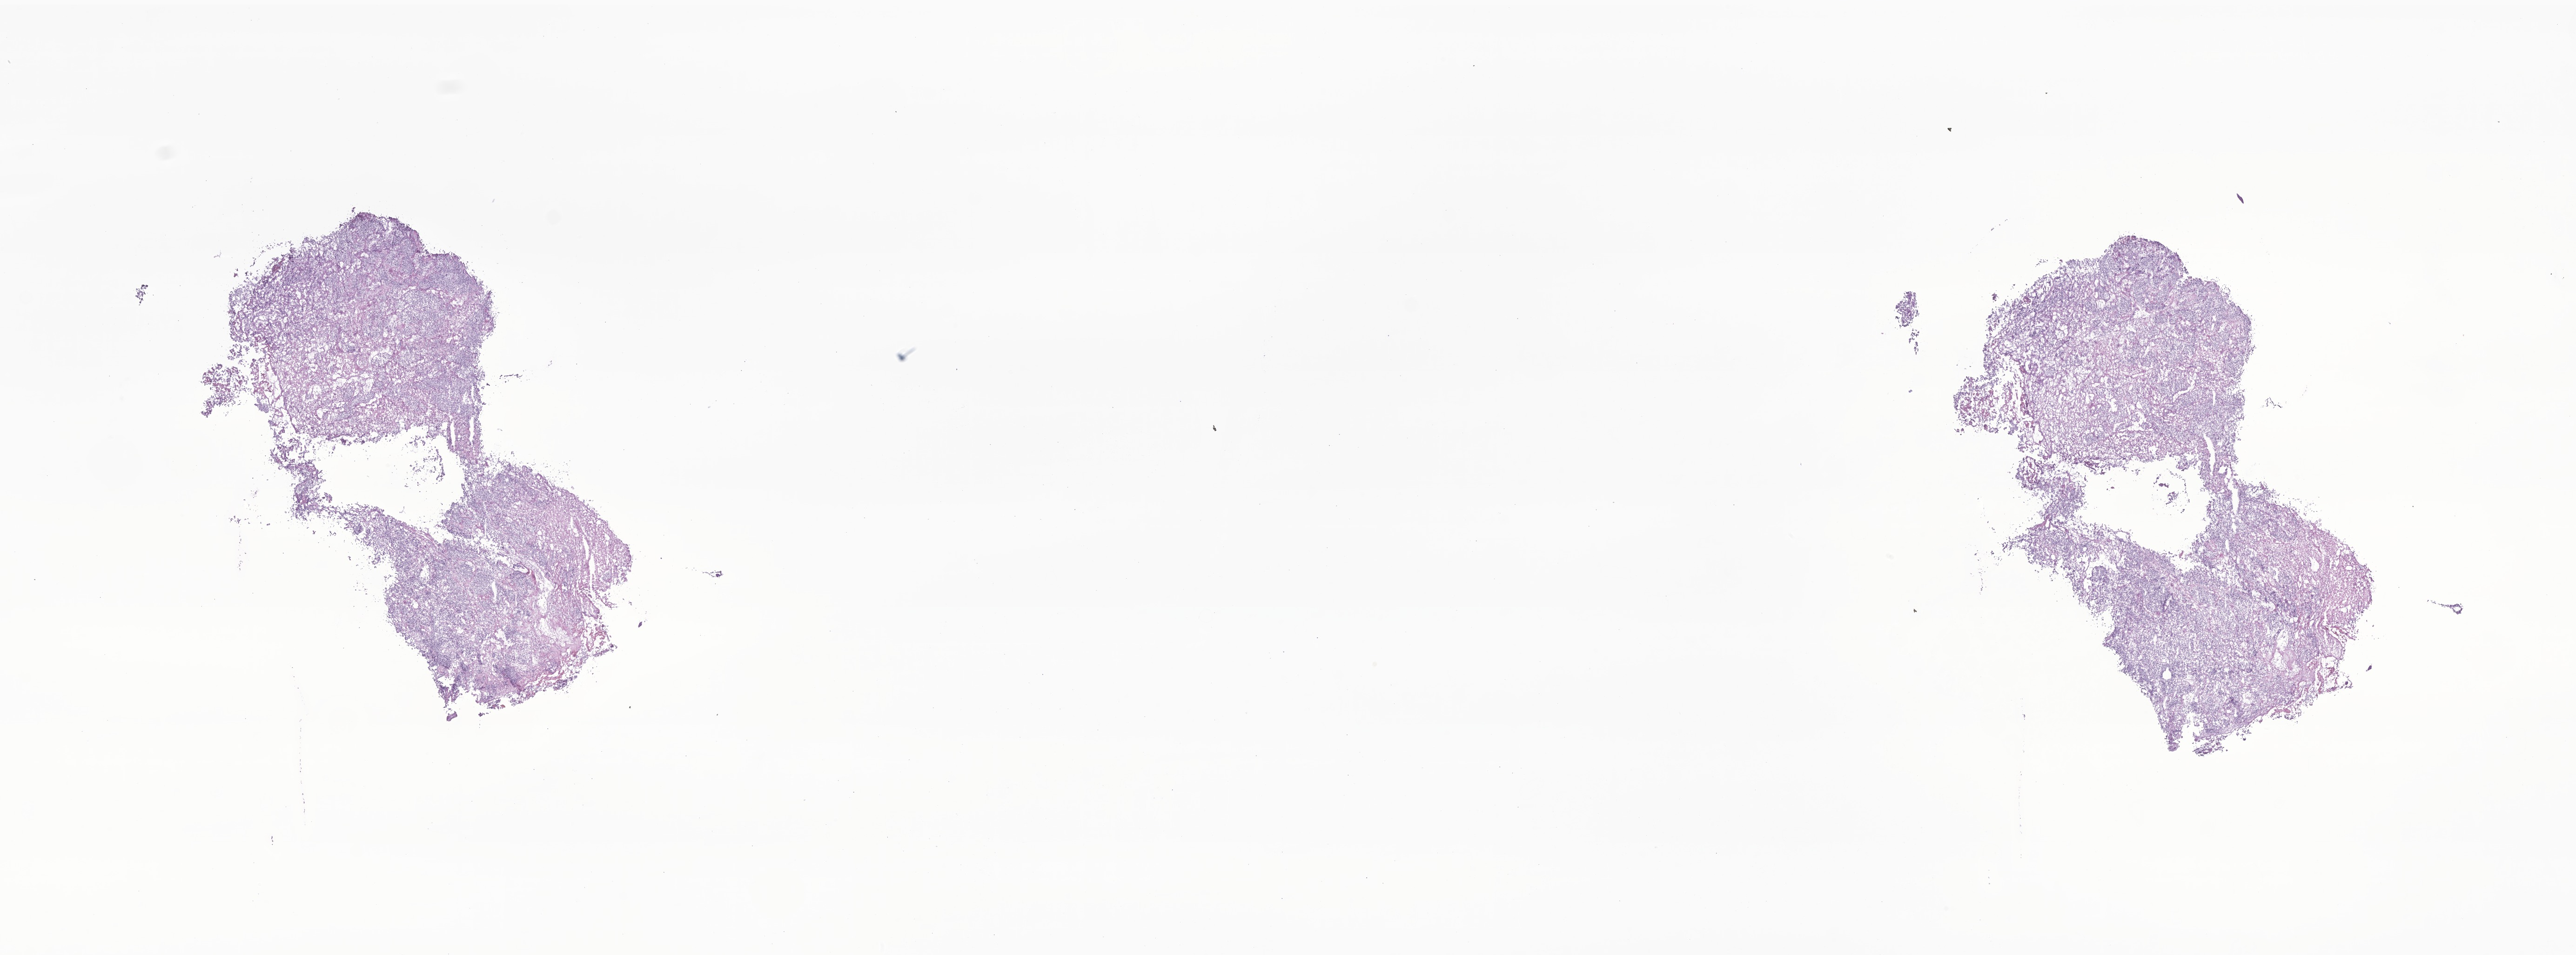
Hematoxylin and eosin (H&E) whole-slide image of tumor tissue from the retroperitoneum, whole scanned area (about 23.3 x 8.7 mm) shown as a low-resolution overview. Frozen section. Patient: male, age 735 days (about 2.0 years).
Diagnosis: Neuroblastoma, NOS.